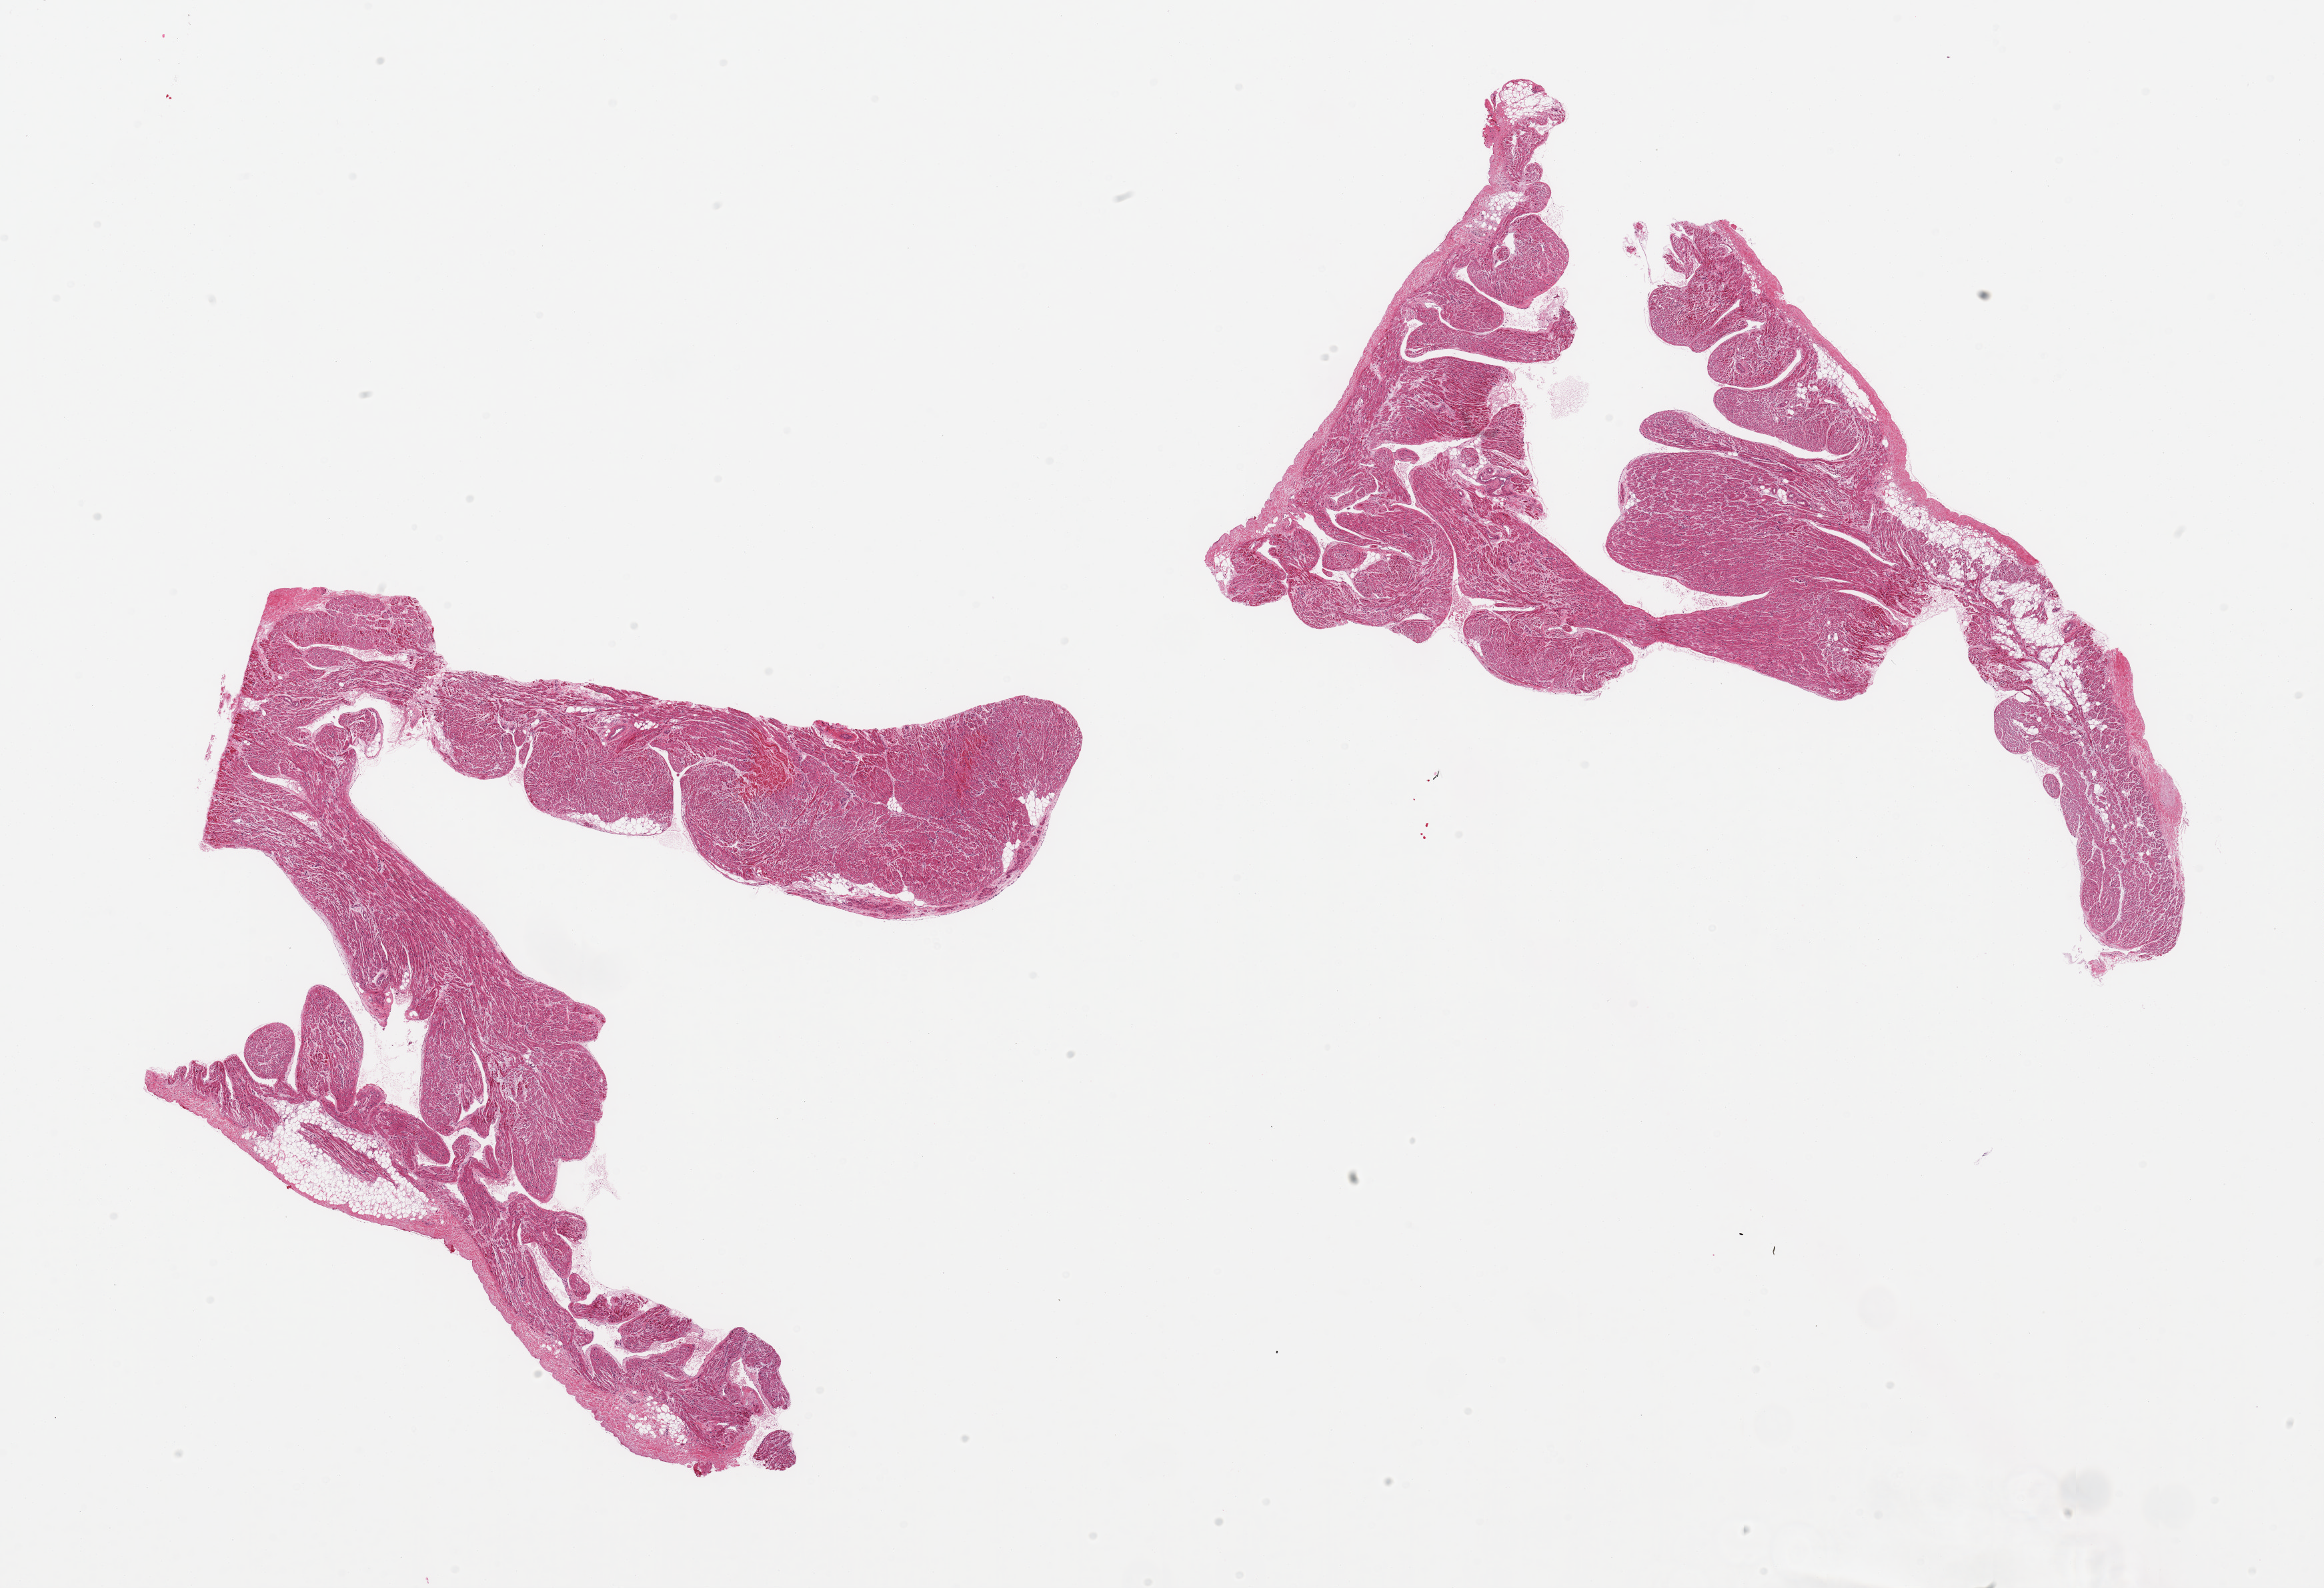
Digitized haematoxylin and eosin-stained section, a low-resolution overview of the entire scanned area, about 27.6 x 18.8 mm; PAXgene-fixed, paraffin-embedded tissue; target tissue: auricular appendage; donor tissue sample.
Reviewer comment on this tissue sample: 2 pieces; 10% internal fat.